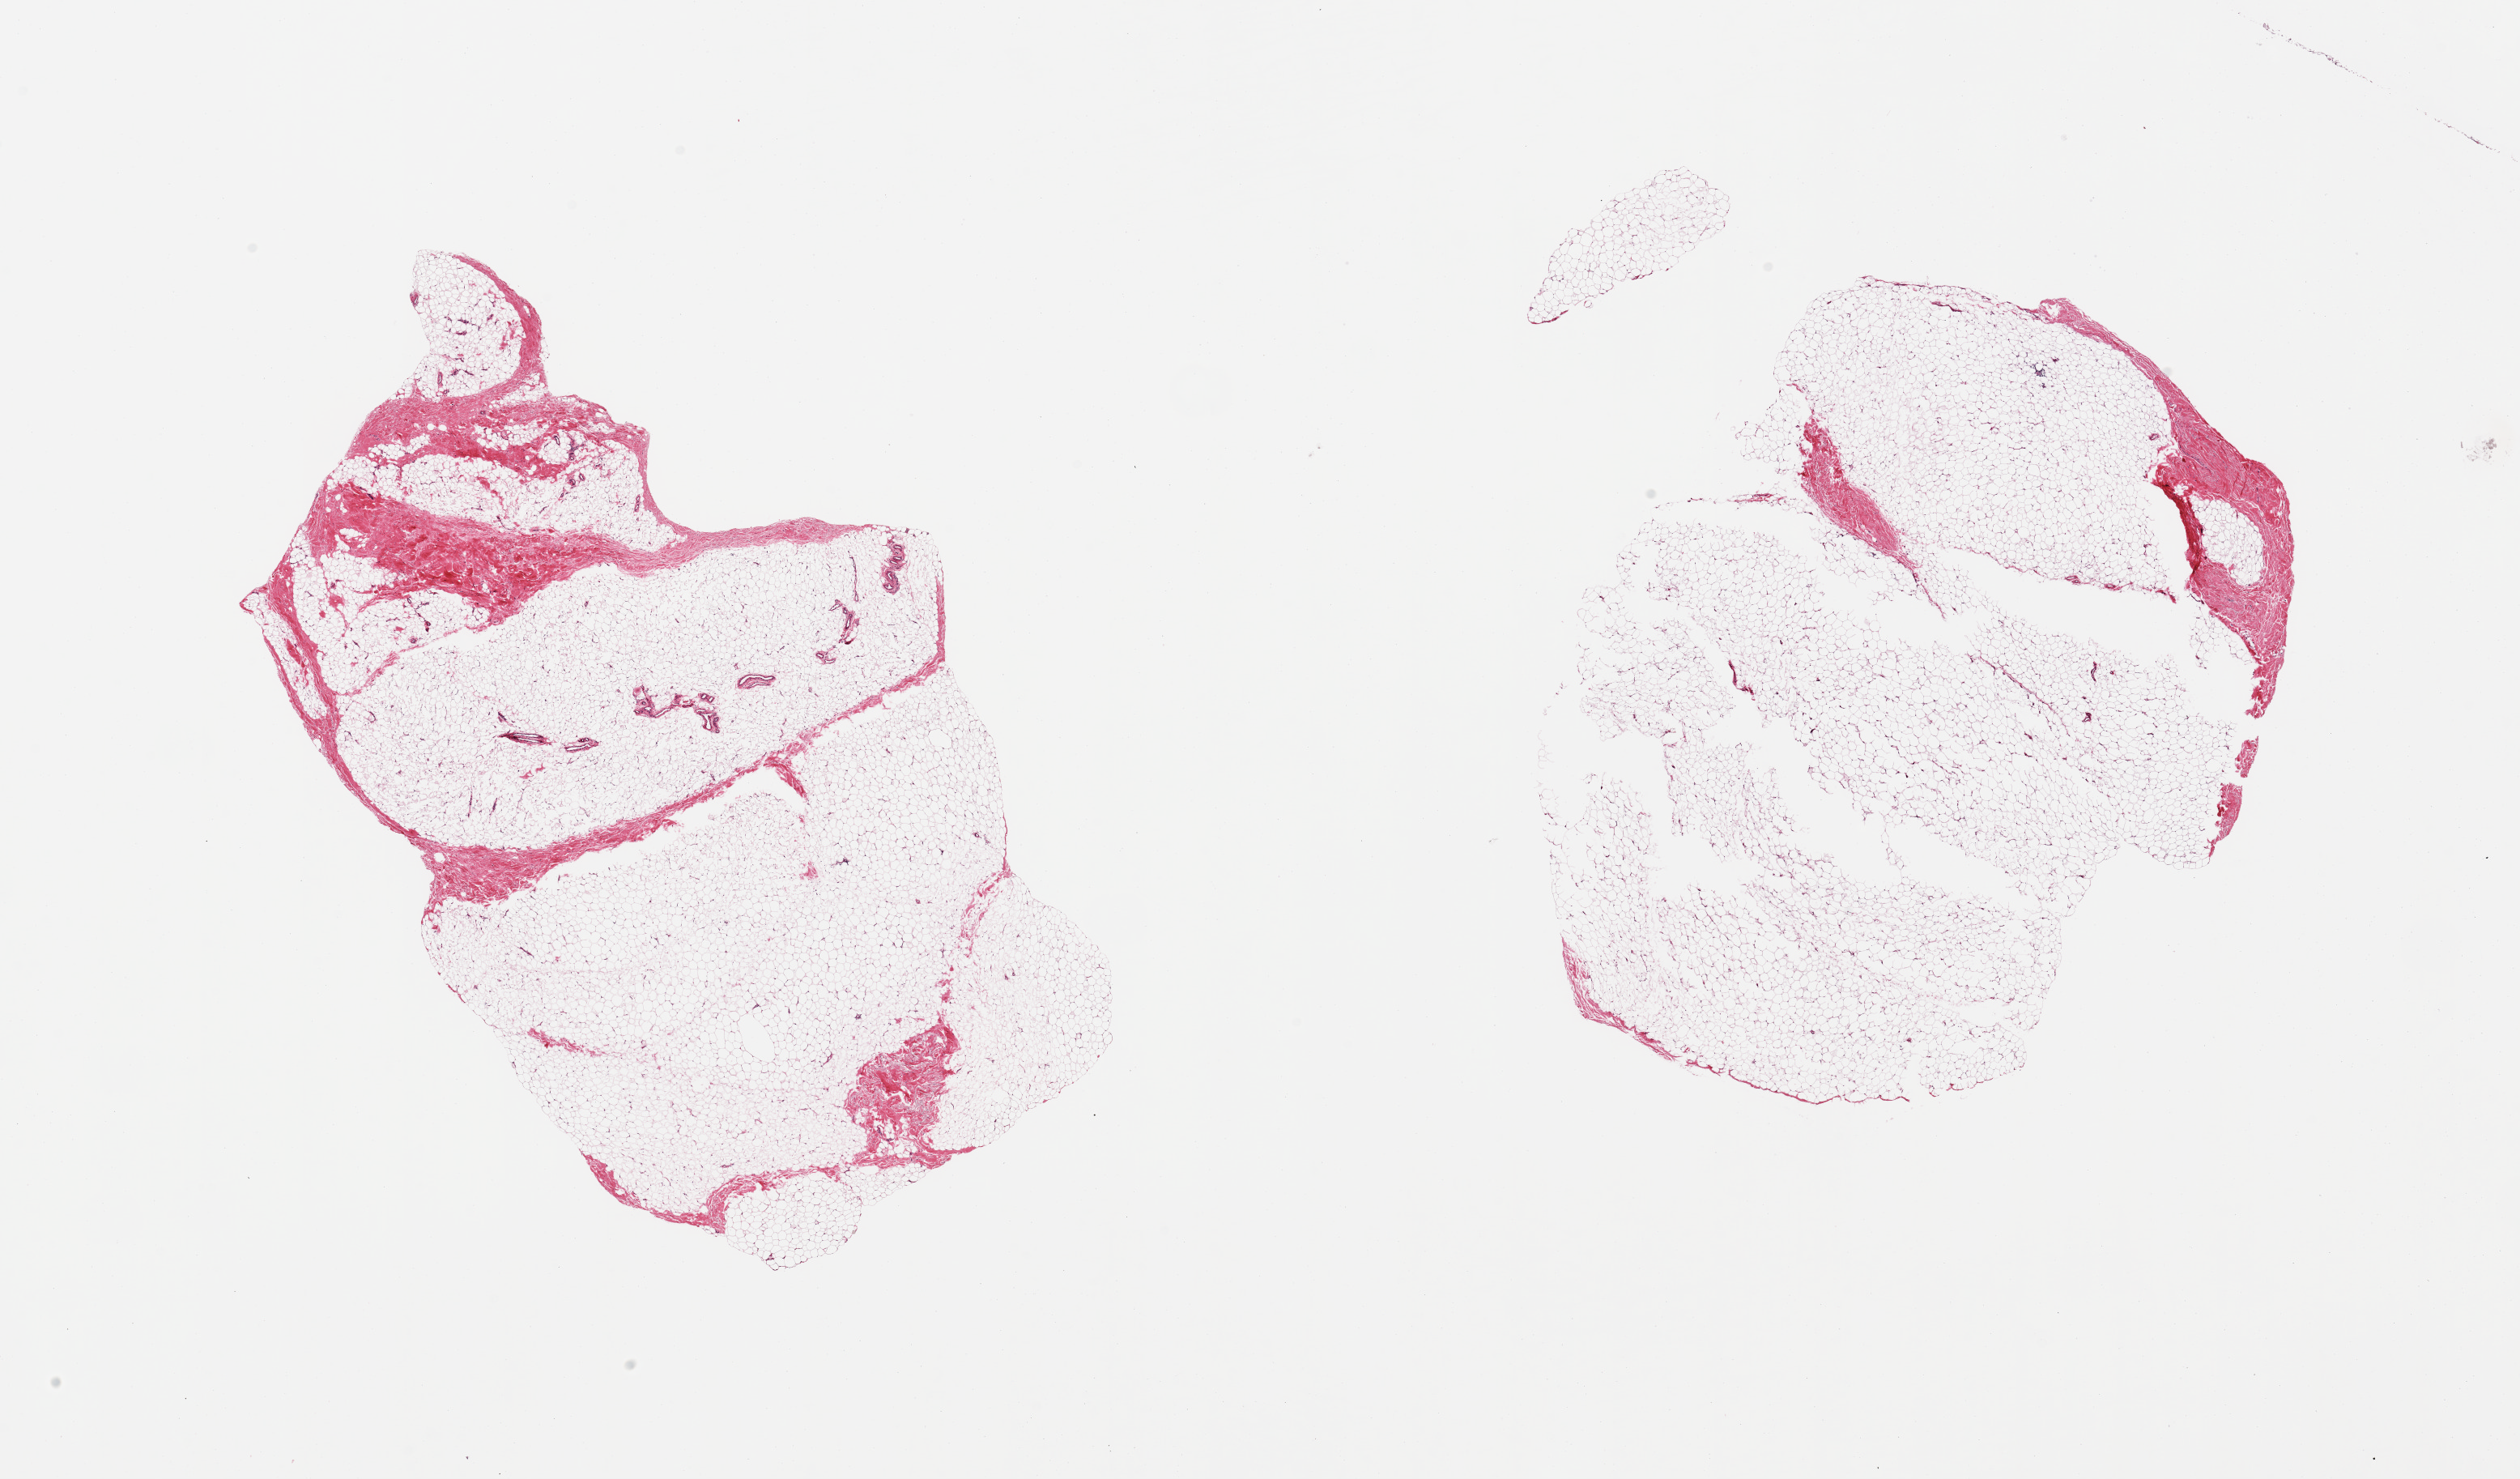
Whole-slide image, H&E stain, brightfield — shown as a low-resolution overview of the whole scanned area (about 24.6 x 14.4 mm, acquisition: 20x scan). PAXgene-fixed paraffin-embedded (PFPE) section. Section of breast (target tissue). Donor tissue sample. Donor sex: male.
- pathologist's review note for this sample: 2 pieces; fibrofatty tissue, no ducts